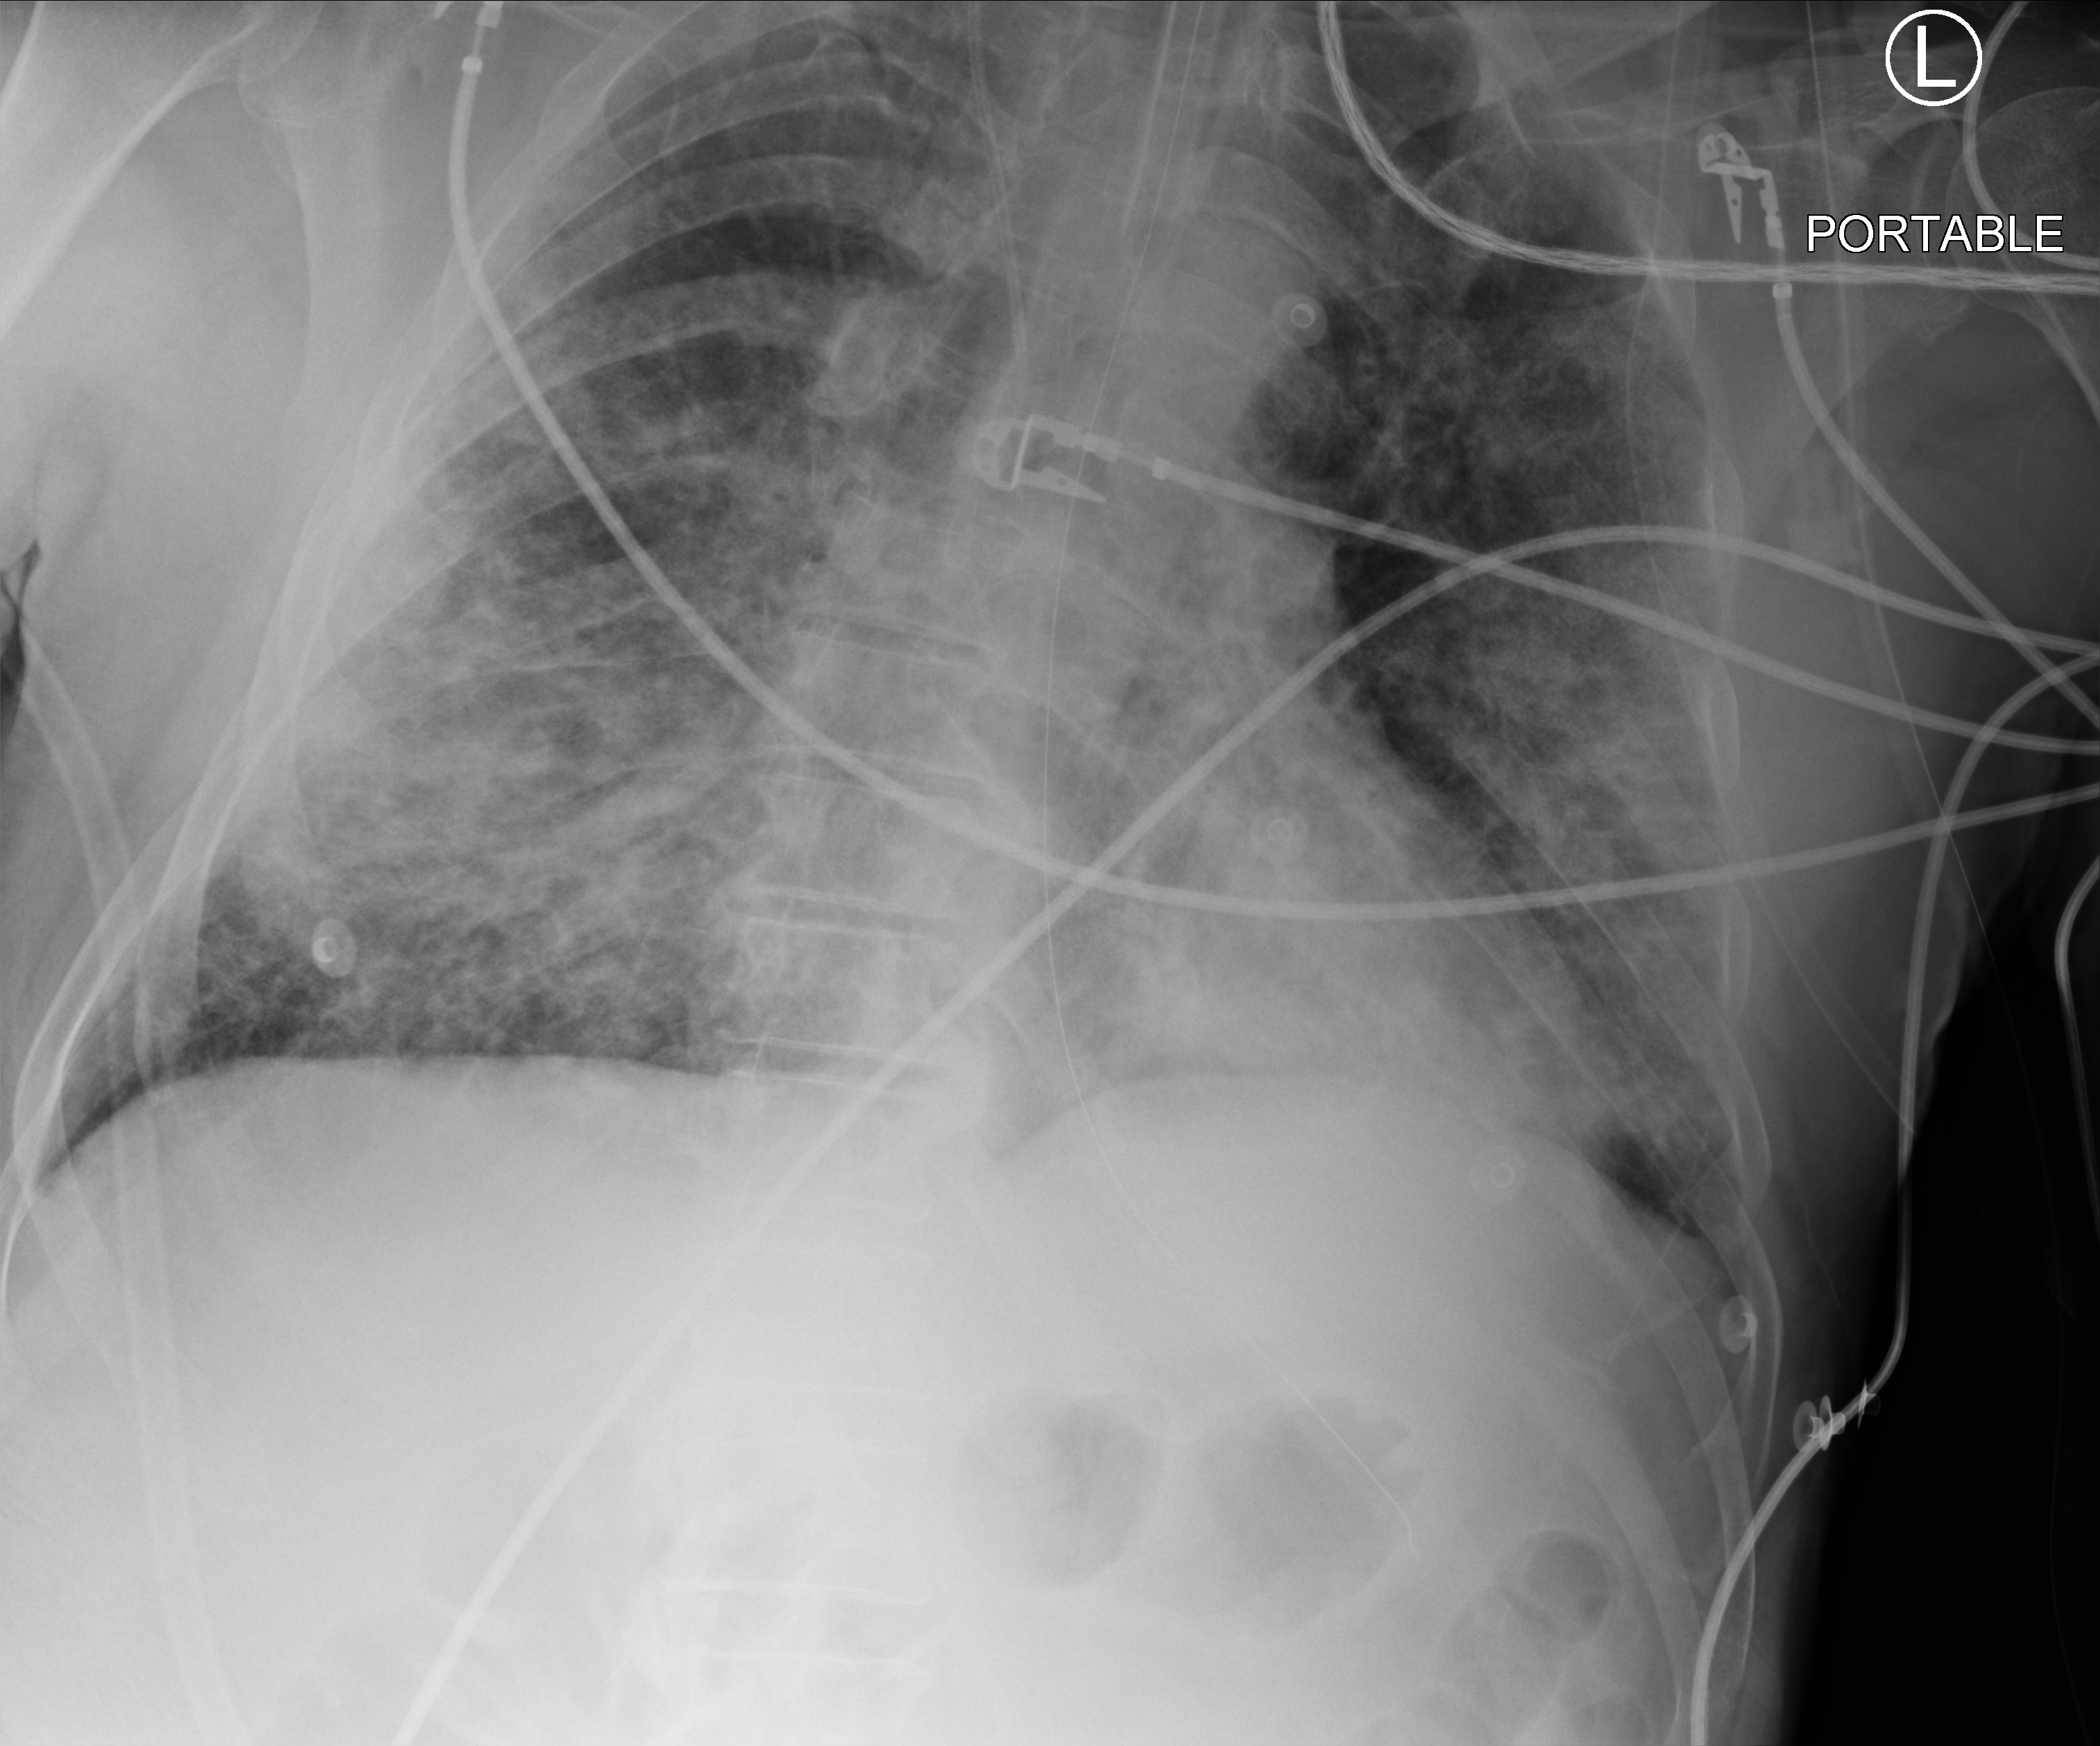
Chest X-ray (portable), anteroposterior (AP) projection. Male patient hospitalised with COVID-19, age 60–74 years.
Admission-level facts for this patient (not findings on this image; timing relative to this image not recorded):
- diabetes (admission record): yes
- mechanically ventilated during this hospital stay: yes
- length of hospital stay: 32 days